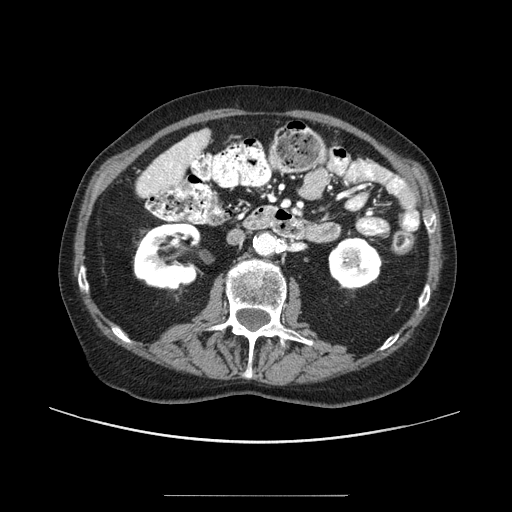
Contrast-enhanced abdominal CT (liver protocol), one axial slice; slice 28 of 91 in the series (ordered by position); reconstruction kernel STANDARD; 100 kVp; one of 2 acquisitions stored at this slice position; soft-tissue window (W 400 / L 40 HU); 2.5 mm slice thickness; 512 × 512 image matrix, field of view 400 × 400 mm. Case-level facts recorded for this patient, not image findings: diagnosis: hepatocellular carcinoma (patient treated with transarterial chemoembolisation; whether this scan precedes or follows treatment is not stated here); TNM stage (as recorded): Stage-I; Child-Pugh class: A; tumour nodularity: uninodular.
Outlined on this slice (semi-automatic segmentation, software-assisted and operator-edited):
- liver parenchyma outside the tumour (the mass and vessels are separate outlines, so this box may not span the whole liver): bounding box <150,129,210,182> (left, top, right, bottom; pixels)
- liver vessels: <164,143,197,175>